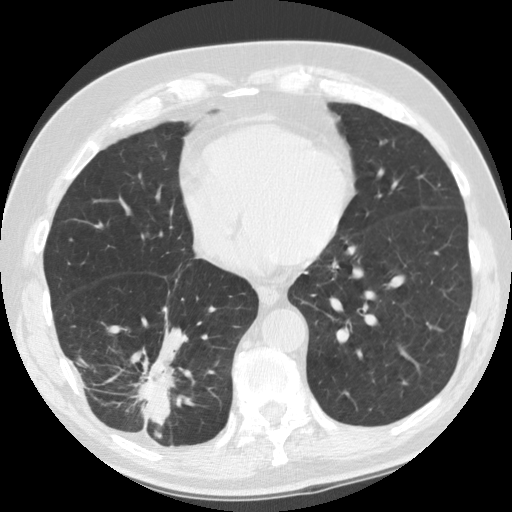
Chest CT (low-dose screening protocol), one axial image. First (baseline) screen. Lung window (W 1500 / L -600 HU). Slice 94 of 135 in the series. Male participant, aged 69 years at enrolment. Former smoker at enrolment.
Expert reader's lesion annotation, bounding box (x1, y1, x2, y2) in pixels: (103, 330, 189, 439). The screening reader recorded 2 non-calcified nodules or masses ≥4 mm on this exam; which of them this box marks is not recorded. Official screen result: positive, change unspecified: nodule(s) >= 4 mm or enlarging nodule(s), mass(es), or other non-specific abnormalities suspicious for lung cancer. Participant outcome: lung cancer diagnosed 40 days after this screen — adenocarcinoma, NOS, right lower lobe, stage IIB (AJCC 6th edition), 45 mm at pathology.